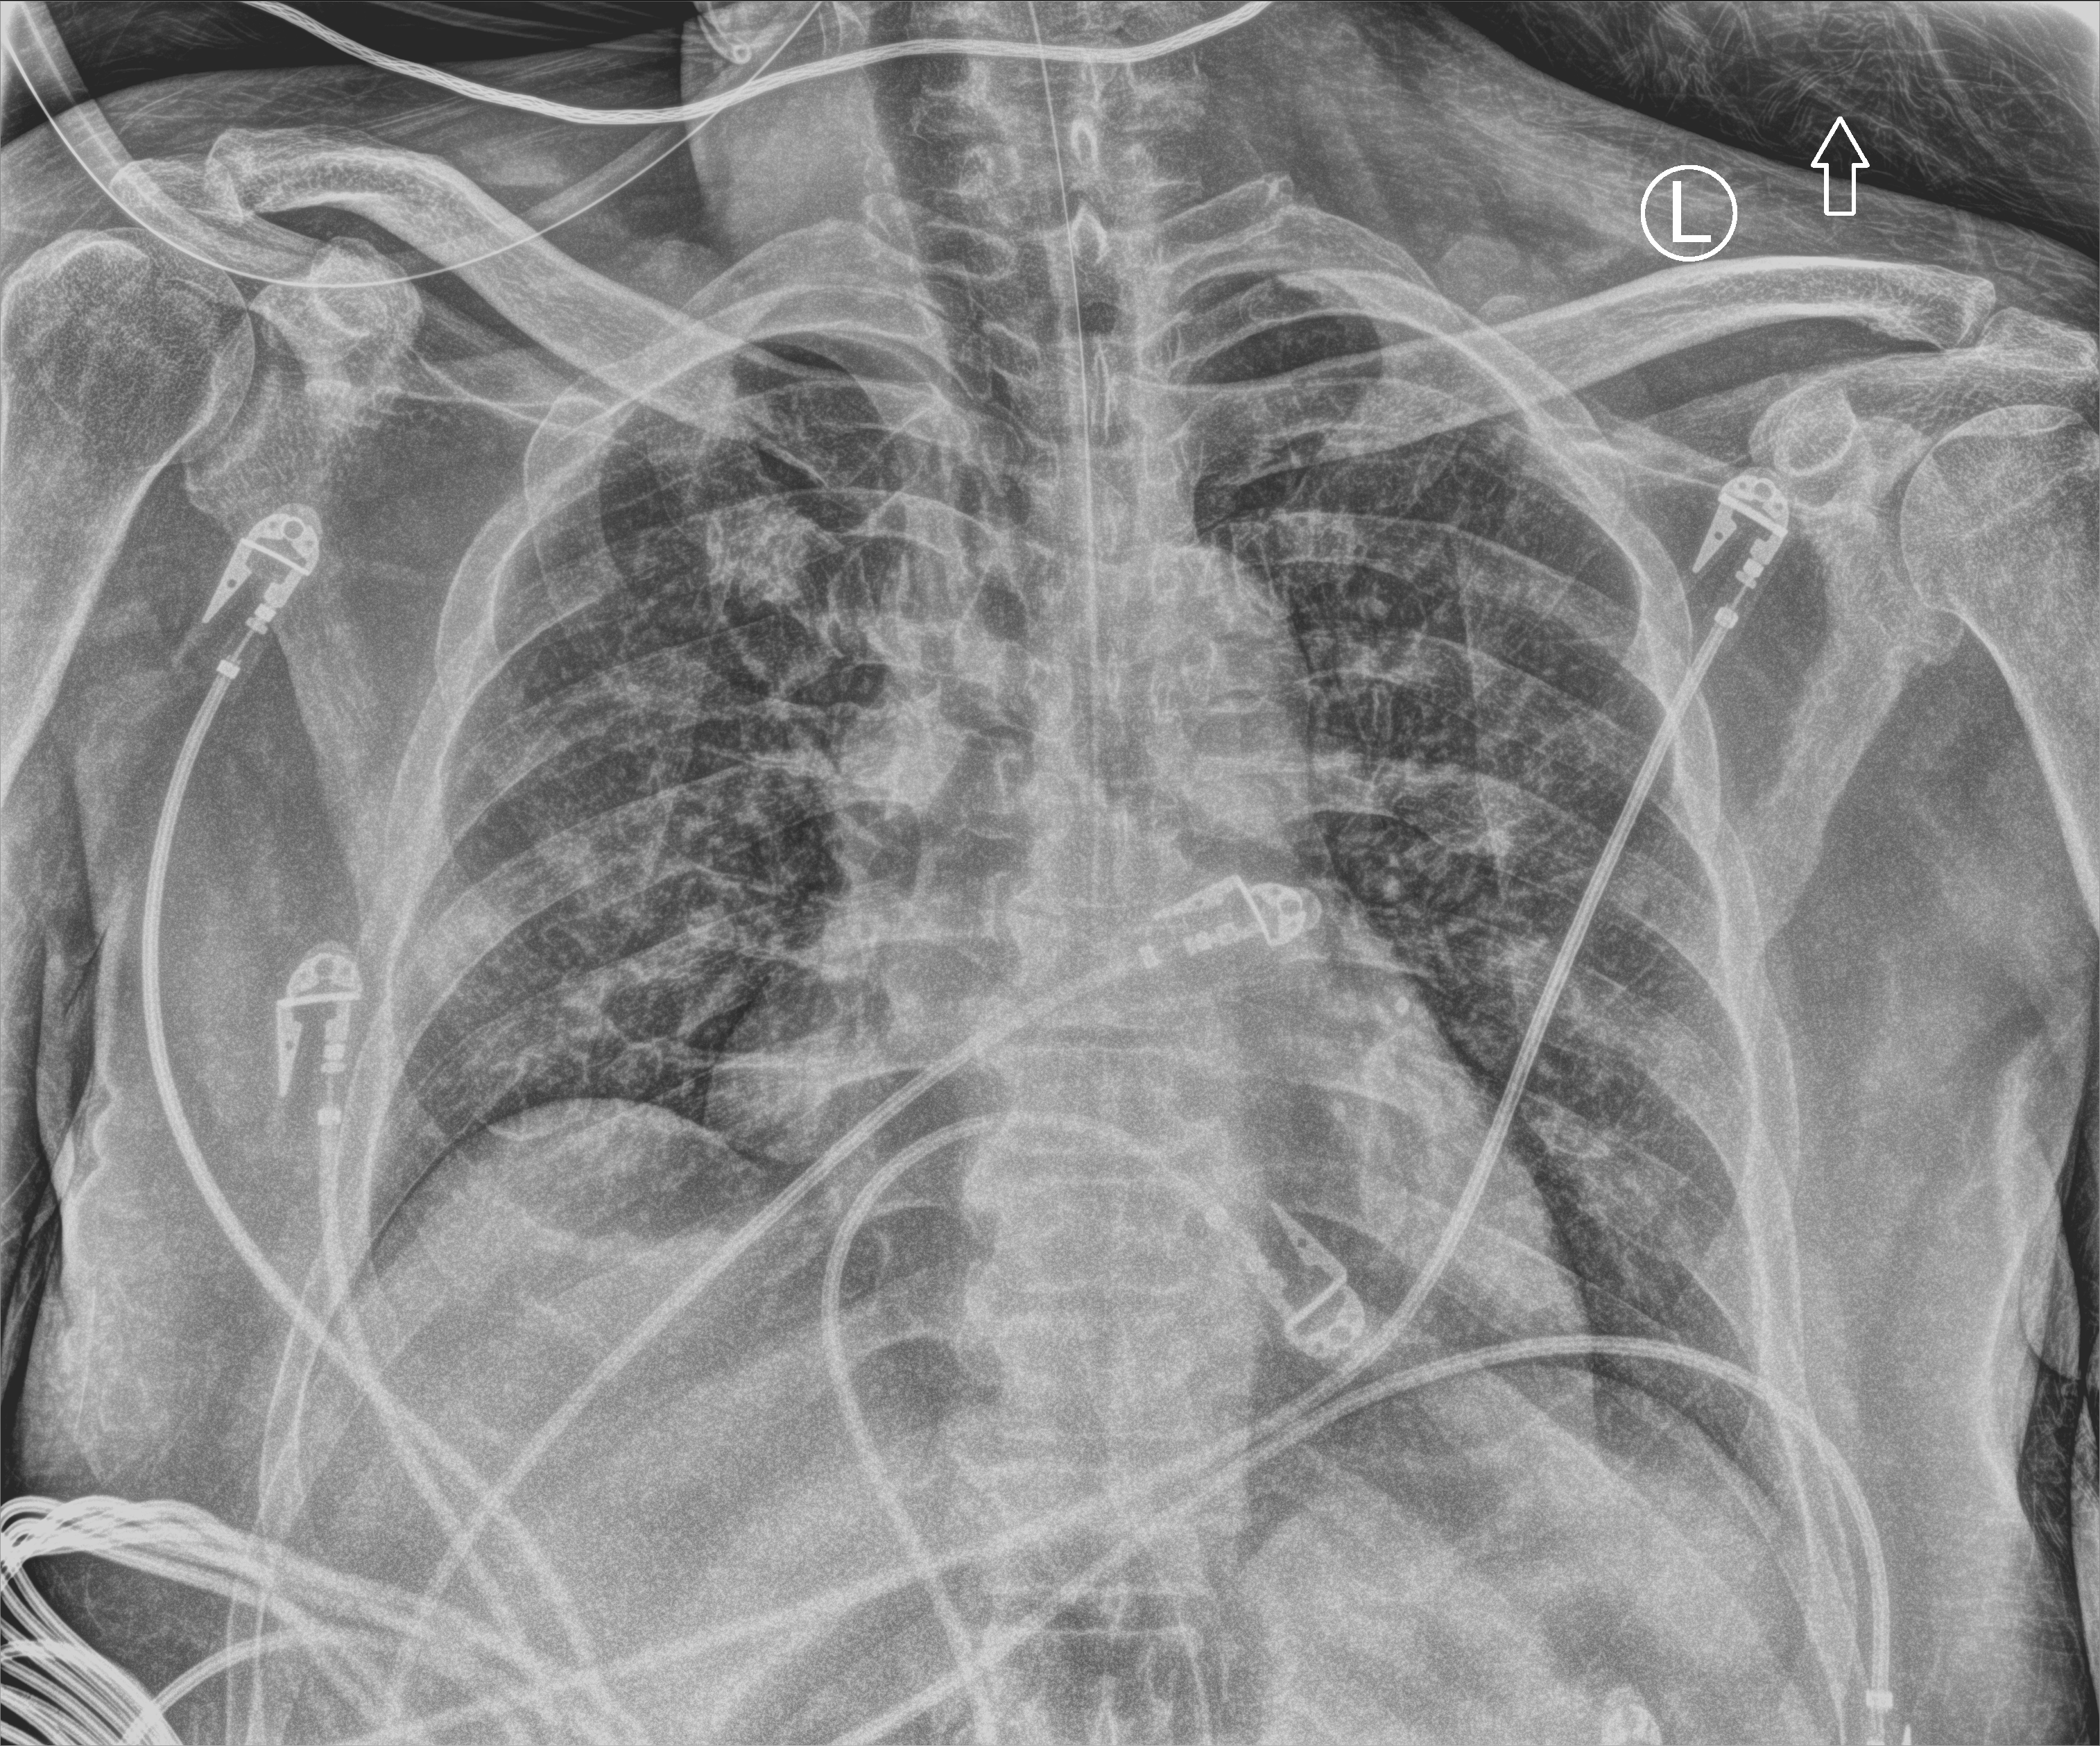
Chest X-ray (portable), anteroposterior (AP) projection. Patient hospitalised with COVID-19, aged 18–59 years.
Admission-level facts for this patient (not findings on this image; timing relative to this image not recorded): length of hospital stay: 37 days; admitted to intensive care during this hospital stay: yes.